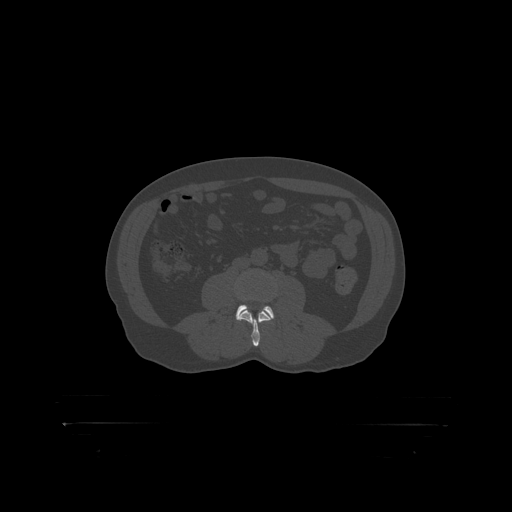
CT including the spine, one axial slice. Position 253 of 399 along the scan axis. Reconstruction kernel STANDARD. 120 kVp. Bone window (W 1800 / L 400 HU). 1.25 mm slice thickness. 512 × 512 image matrix. Patient: male, 46 years. Case-level facts recorded for this patient, not image findings: primary cancer: skin.
Annotated regions visible in this slice (semi-automatically segmented with operator editing):
- L3 vertebra: bounding box (x1, y1, x2, y2) in pixels: (240, 309, 270, 319)
- L4 vertebra: (236, 305, 274, 317)